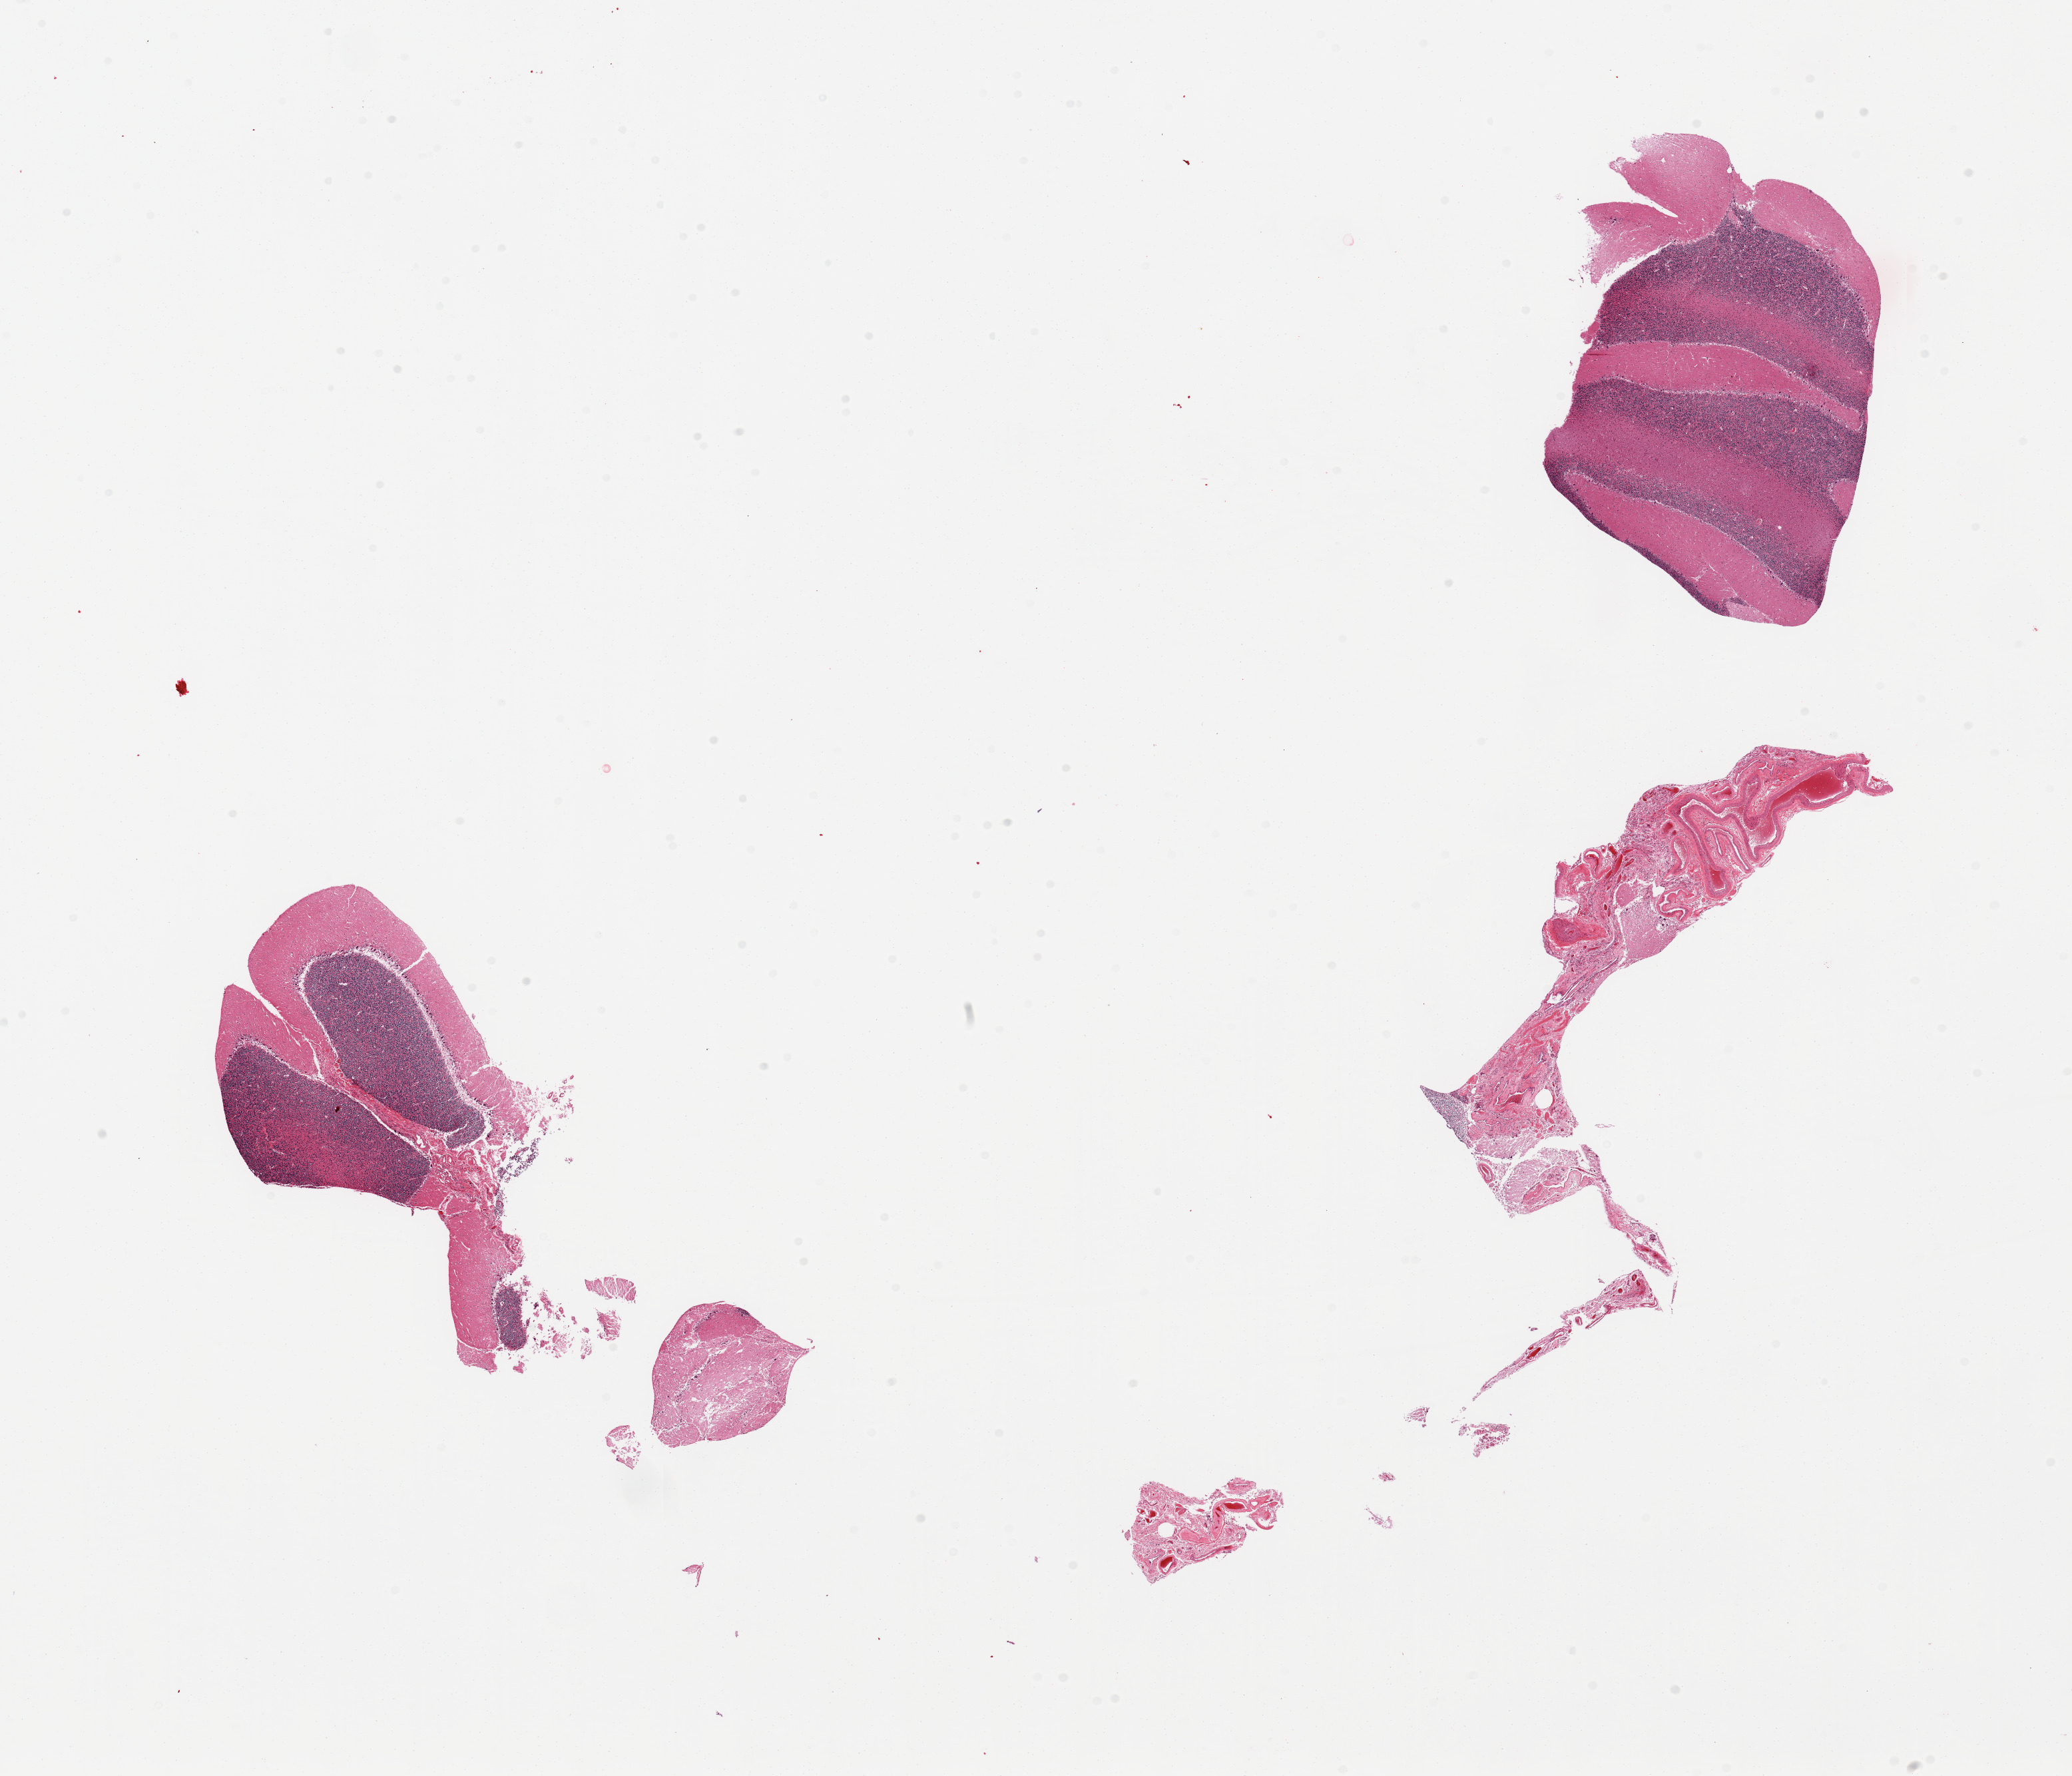
Hematoxylin and eosin (H&E) whole-slide image, whole scanned area (about 24.6 x 21.1 mm, slide scanned at 20x) shown as a low-resolution overview; PAXgene-fixed paraffin-embedded (PFPE) section; target tissue: cerebellum; donor tissue sample.
Reviewer comment on this tissue sample: 2 pieces (fragmented).